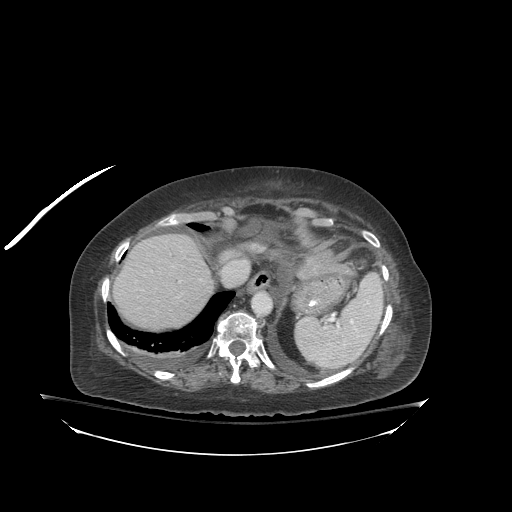
Contrast-enhanced abdominal CT (liver protocol), one axial slice; position 69 of 81 along the scan axis; reconstruction kernel STANDARD; soft-tissue window (W 400 / L 40 HU); 2.5 mm slice thickness; 512 × 512 image matrix, field of view 500 × 500 mm. Case-level facts recorded for this patient, not image findings: diagnosis: hepatocellular carcinoma (patient treated with transarterial chemoembolisation; whether this scan precedes or follows treatment is not stated here); TNM stage (as recorded): Stage-I; Child-Pugh class: B; tumour differentiation: well-moderately differentiated; tumour nodularity: uninodular.
Outlined on this slice (semi-automatically segmented with operator editing):
- abdominal aorta: bounding box [x1, y1, x2, y2] px = [253, 293, 272, 315]
- liver parenchyma outside the tumour (the mass and vessels are separate outlines, so this box may not span the whole liver): [124, 234, 214, 326]